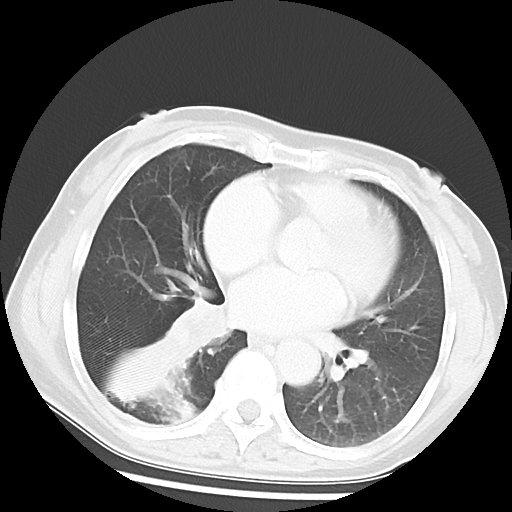
Chest CT, one axial slice. Lung window (W 1500 / L -600 HU). 512 × 512 image matrix, field of view 297 × 297 mm. Female patient, age 54 years. Case-level facts recorded for this patient, not image findings: clinical TNM (as recorded): T1c N0 M0; histopathological grade: G1-2.
Outlined on this slice (bounding box drawn by a radiologist):
- lung tumour (recorded histology: squamous cell carcinoma): bounding box [x1, y1, x2, y2] px = [160, 289, 233, 361]